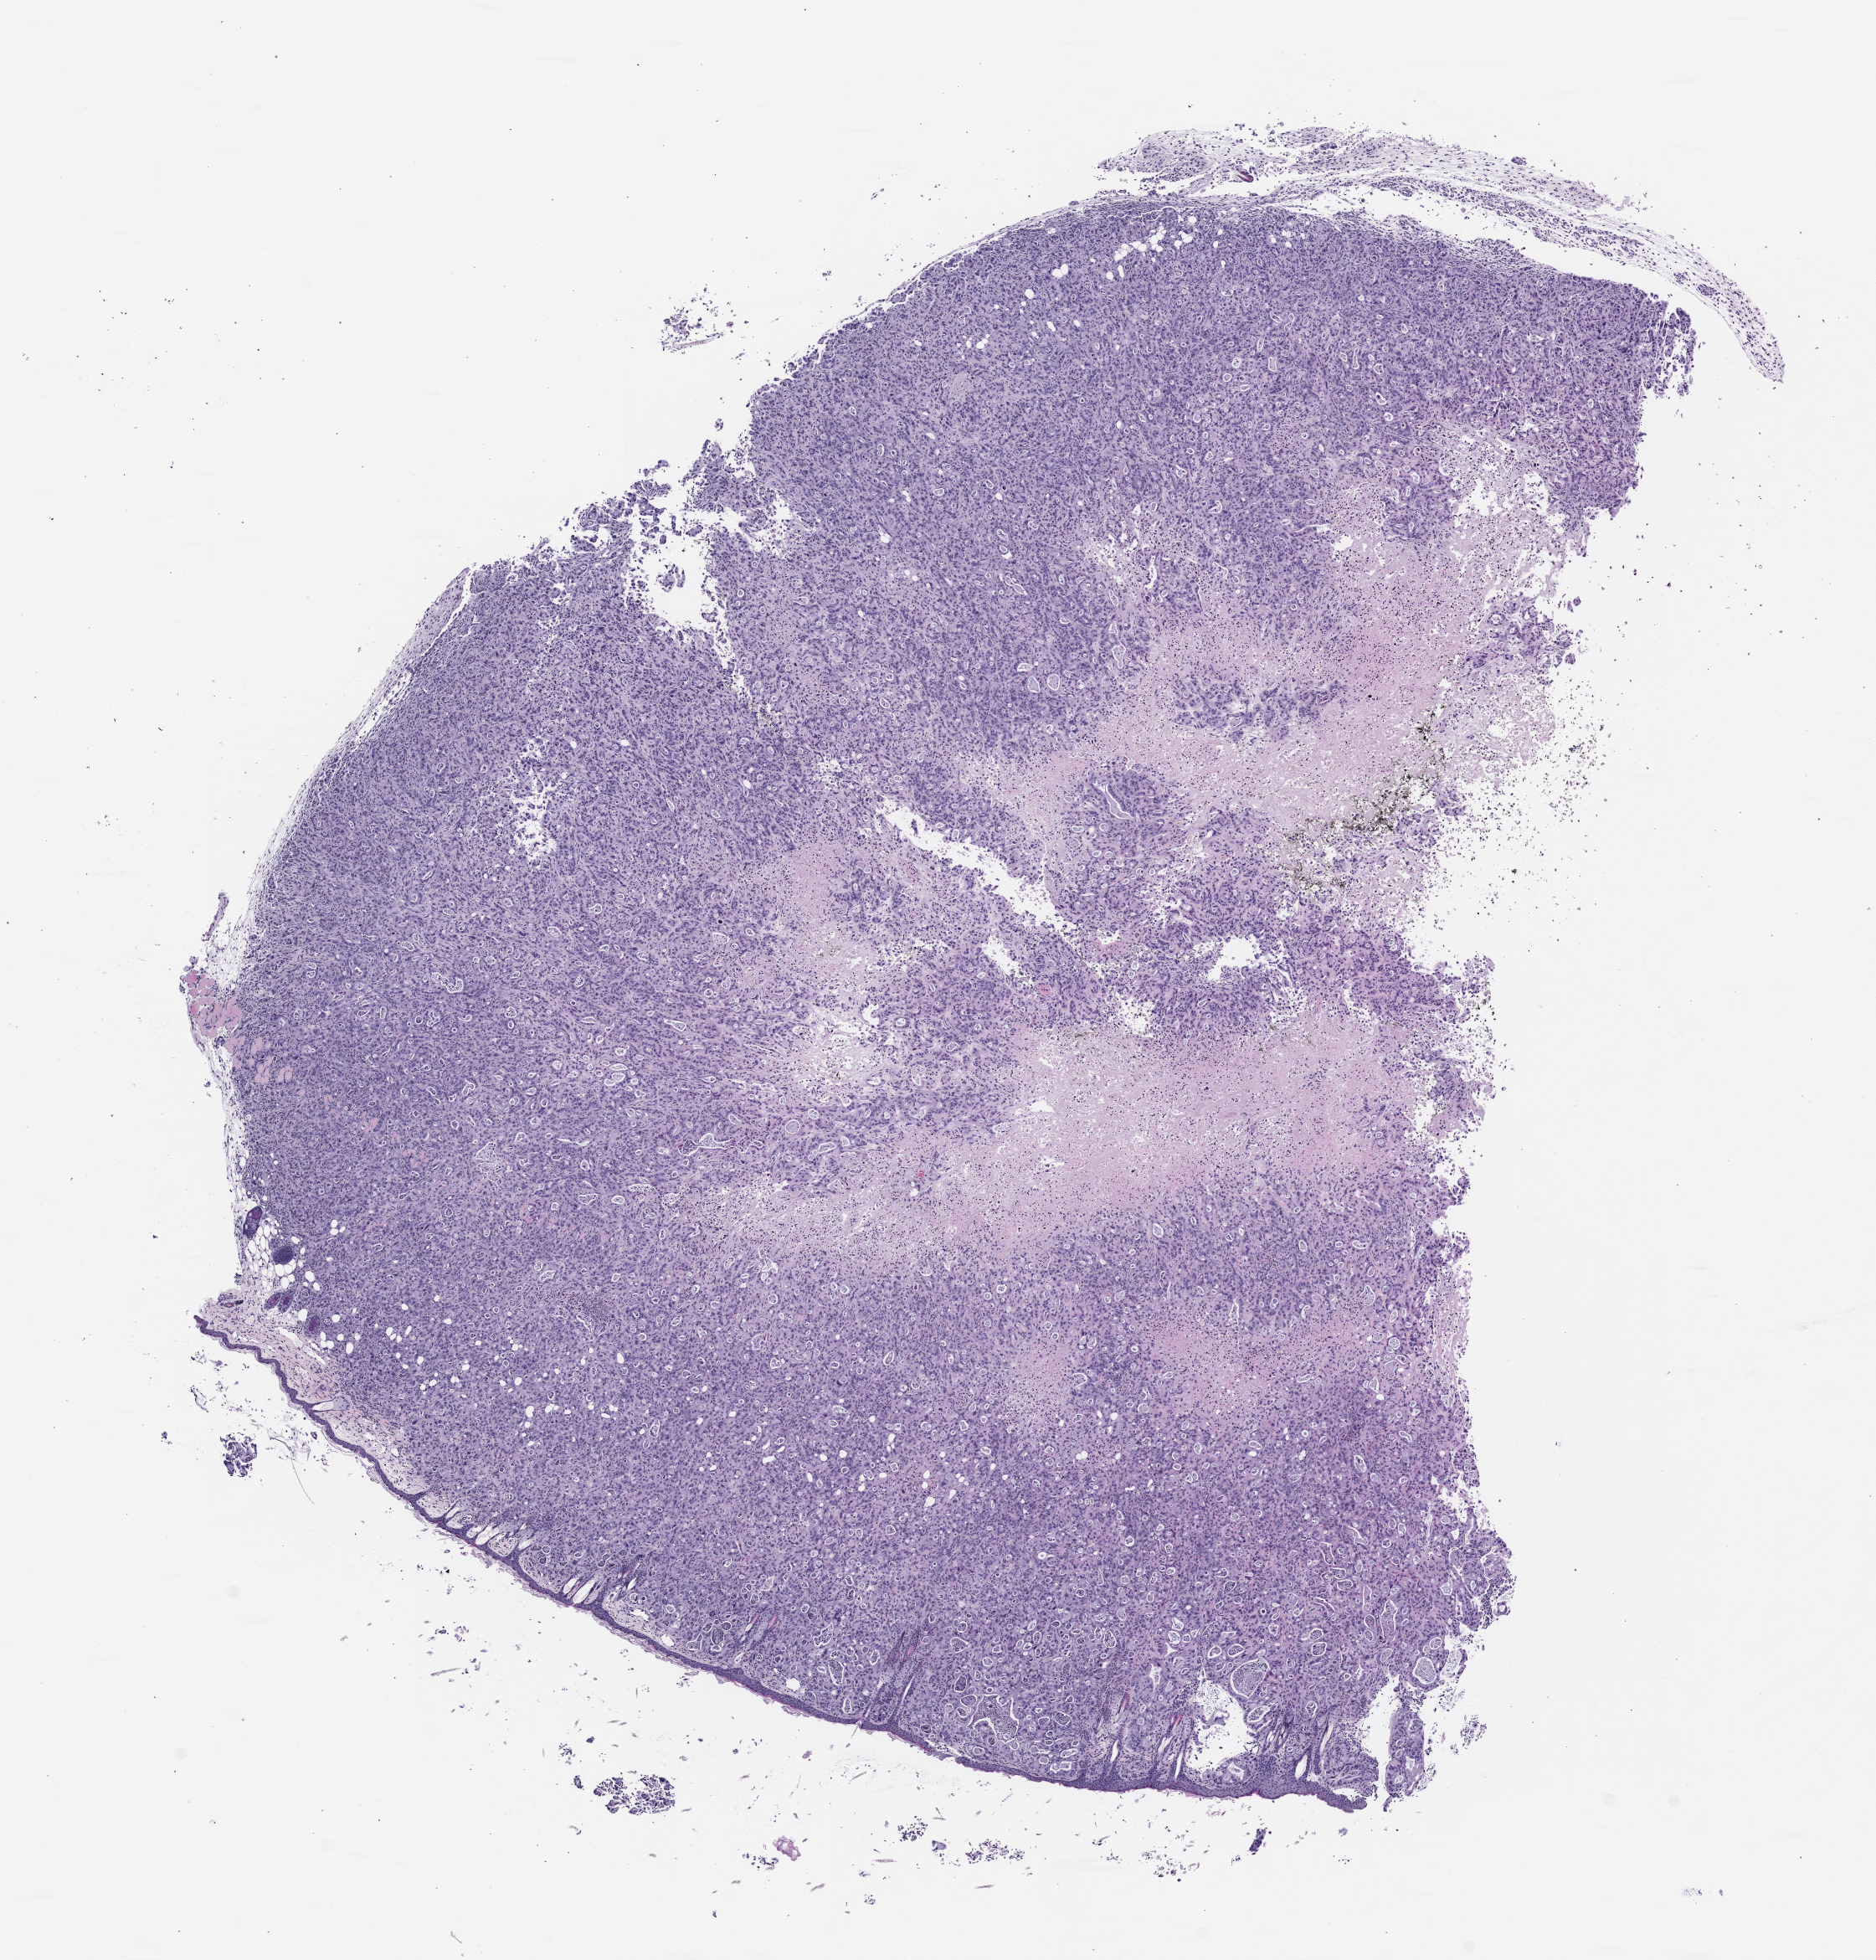
Whole-slide image, H&E: patient-derived xenograft (human tumor grown in a mouse), passage 2, a low-resolution overview of the entire scanned area, about 9.0 x 9.4 mm; FFPE section; tumor site category: pancreas.
Originating patient diagnosis: Pancreatic Adenocarcinoma.